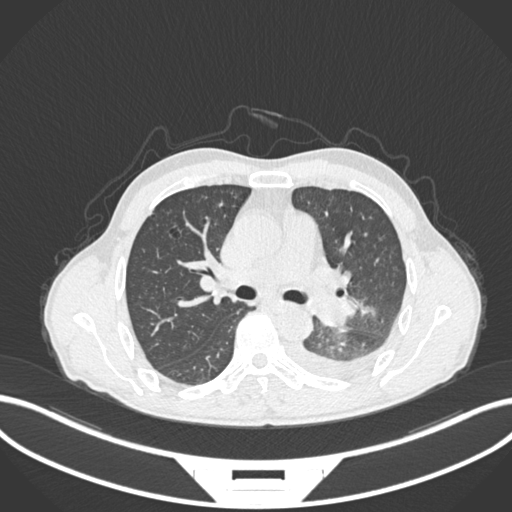
Chest CT, one axial slice. 120 kVp. Lung window (W 1500 / L -600 HU). 1 mm slice thickness. 512 × 512 image matrix, field of view 400 × 400 mm. Male patient, age 47 years. Case-level facts recorded for this patient, not image findings: clinical TNM (as recorded): T3 N1 M1c; histopathological grade: G3.
Annotated regions visible in this slice (bounding box drawn by a radiologist):
- lung tumour (recorded histology: small cell carcinoma): box from (x=316, y=296) to (x=360, y=327) px